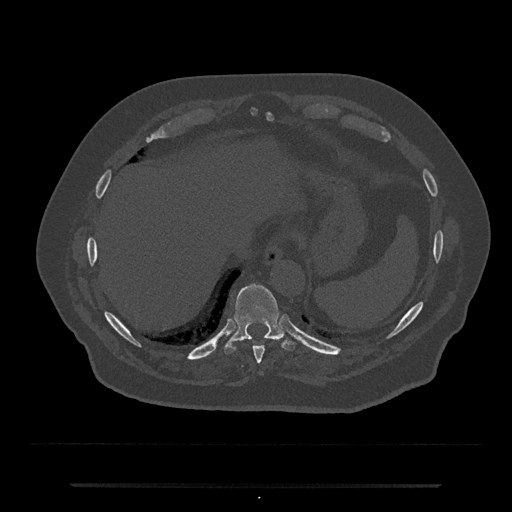
CT including the spine, one axial slice. Reconstruction kernel Br40s/3. 120 kVp. Bone window (W 1800 / L 400 HU). 0.5 mm slice thickness. 512 × 512 image matrix, field of view 434 × 434 mm. Male patient, age 80 years. Case-level facts recorded for this patient, not image findings: primary cancer: prostate.
Outlined on this slice (semi-automatically segmented with operator editing):
- T10 vertebra: box from (x=223, y=284) to (x=296, y=354) px
- T9 vertebra: (x=253, y=346)–(x=264, y=364)